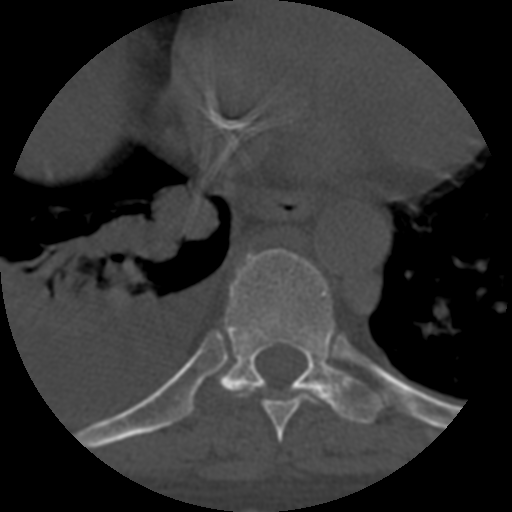
CT including the spine, one axial slice. Slice 384 of 708 in the series (ordered by position). Reconstruction kernel STANDARD. 120 kVp. One of 3 acquisitions stored at this slice position. Bone window (W 1800 / L 400 HU). 1.25 mm slice thickness. 512 × 512 image matrix. Patient age 55 years. Case-level facts recorded for this patient, not image findings: primary cancer: colon; vertebrae with lytic lesions (as recorded): T12, L1, L5.
Annotated regions visible in this slice (semi-automatically segmented with operator editing):
- T8 vertebra: box from (x=262, y=395) to (x=319, y=443) px
- T9 vertebra: (x=216, y=248)–(x=379, y=425)